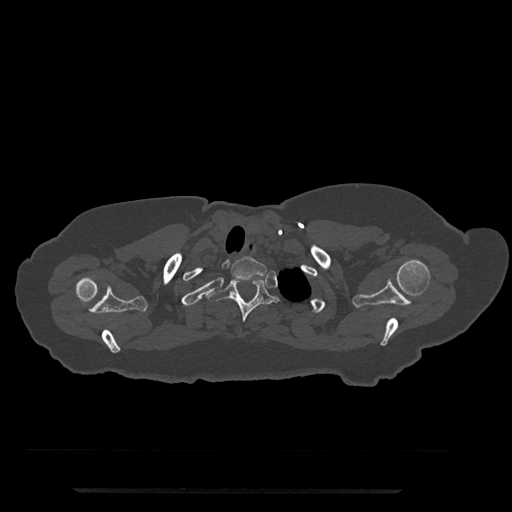
CT including the spine, one axial slice; slice 683 of 797 in the series (ordered by position); reconstruction kernel Br40s/3; 120 kVp; bone window (W 1800 / L 400 HU); 0.5 mm slice thickness; 512 × 512 image matrix. Patient: female, 51 years. Case-level facts recorded for this patient, not image findings: primary cancer: neuro; vertebrae with lytic lesions (as recorded): T8.
Structures marked on this image (semi-automatic segmentation, software-assisted and operator-edited):
- T1 vertebra: bounding box (x1, y1, x2, y2) in pixels: (231, 256, 267, 281)
- T2 vertebra: (206, 277, 279, 322)